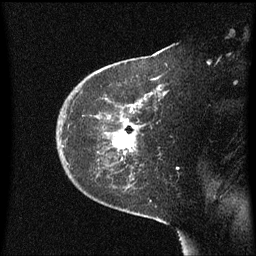
Breast MRI (dynamic contrast-enhanced), one sagittal slice; dynamic contrast-enhanced series, image 2 of 3 at this slice position (ordered by acquisition); 1.5 T; TE 4.2 ms, TR 8.4 ms; 2 mm slice thickness; 256 × 256 image matrix, field of view 200 × 200 mm. Patient: female, 38 years. Case-level facts recorded for this patient, not image findings: setting: breast cancer imaged before/during neoadjuvant chemotherapy; receptor status: HER2-positive.
Annotated regions visible in this slice (semi-automatically segmented with operator editing):
- analysis volume of interest (the breast-tissue region the enhancement analysis was run in; not a lesion): bounding box <57,50,169,185> (left, top, right, bottom; pixels)
- tumour enhancement mask (voxels above the 70 % enhancement threshold inside the analysis volume of interest): <114,110,133,153>